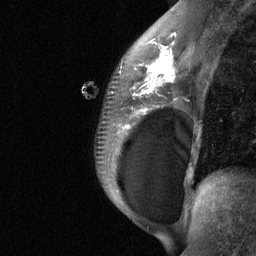
Breast MRI (dynamic contrast-enhanced), one sagittal slice. Slice 41 of 64 in the series (ordered by position). Dynamic contrast-enhanced study with each time point stored as its own series, time point 2 of 3 at this slice position (early post-contrast, ordered by acquisition time). 1.5 T. TE 4.8 ms, TR 27 ms. 256 × 256 image matrix. Patient: female, 34 years. Case-level facts recorded for this patient, not image findings: setting: breast cancer imaged before/during neoadjuvant chemotherapy; receptor status: HR-positive, HER2-negative.
Annotated regions visible in this slice (semi-automatically segmented with operator editing):
- analysis volume of interest (the breast-tissue region the enhancement analysis was run in; not a lesion): bounding box [x1, y1, x2, y2] px = [92, 50, 188, 185]
- tumour enhancement mask (voxels above the 90 % enhancement threshold inside the analysis volume of interest): [133, 50, 175, 114]